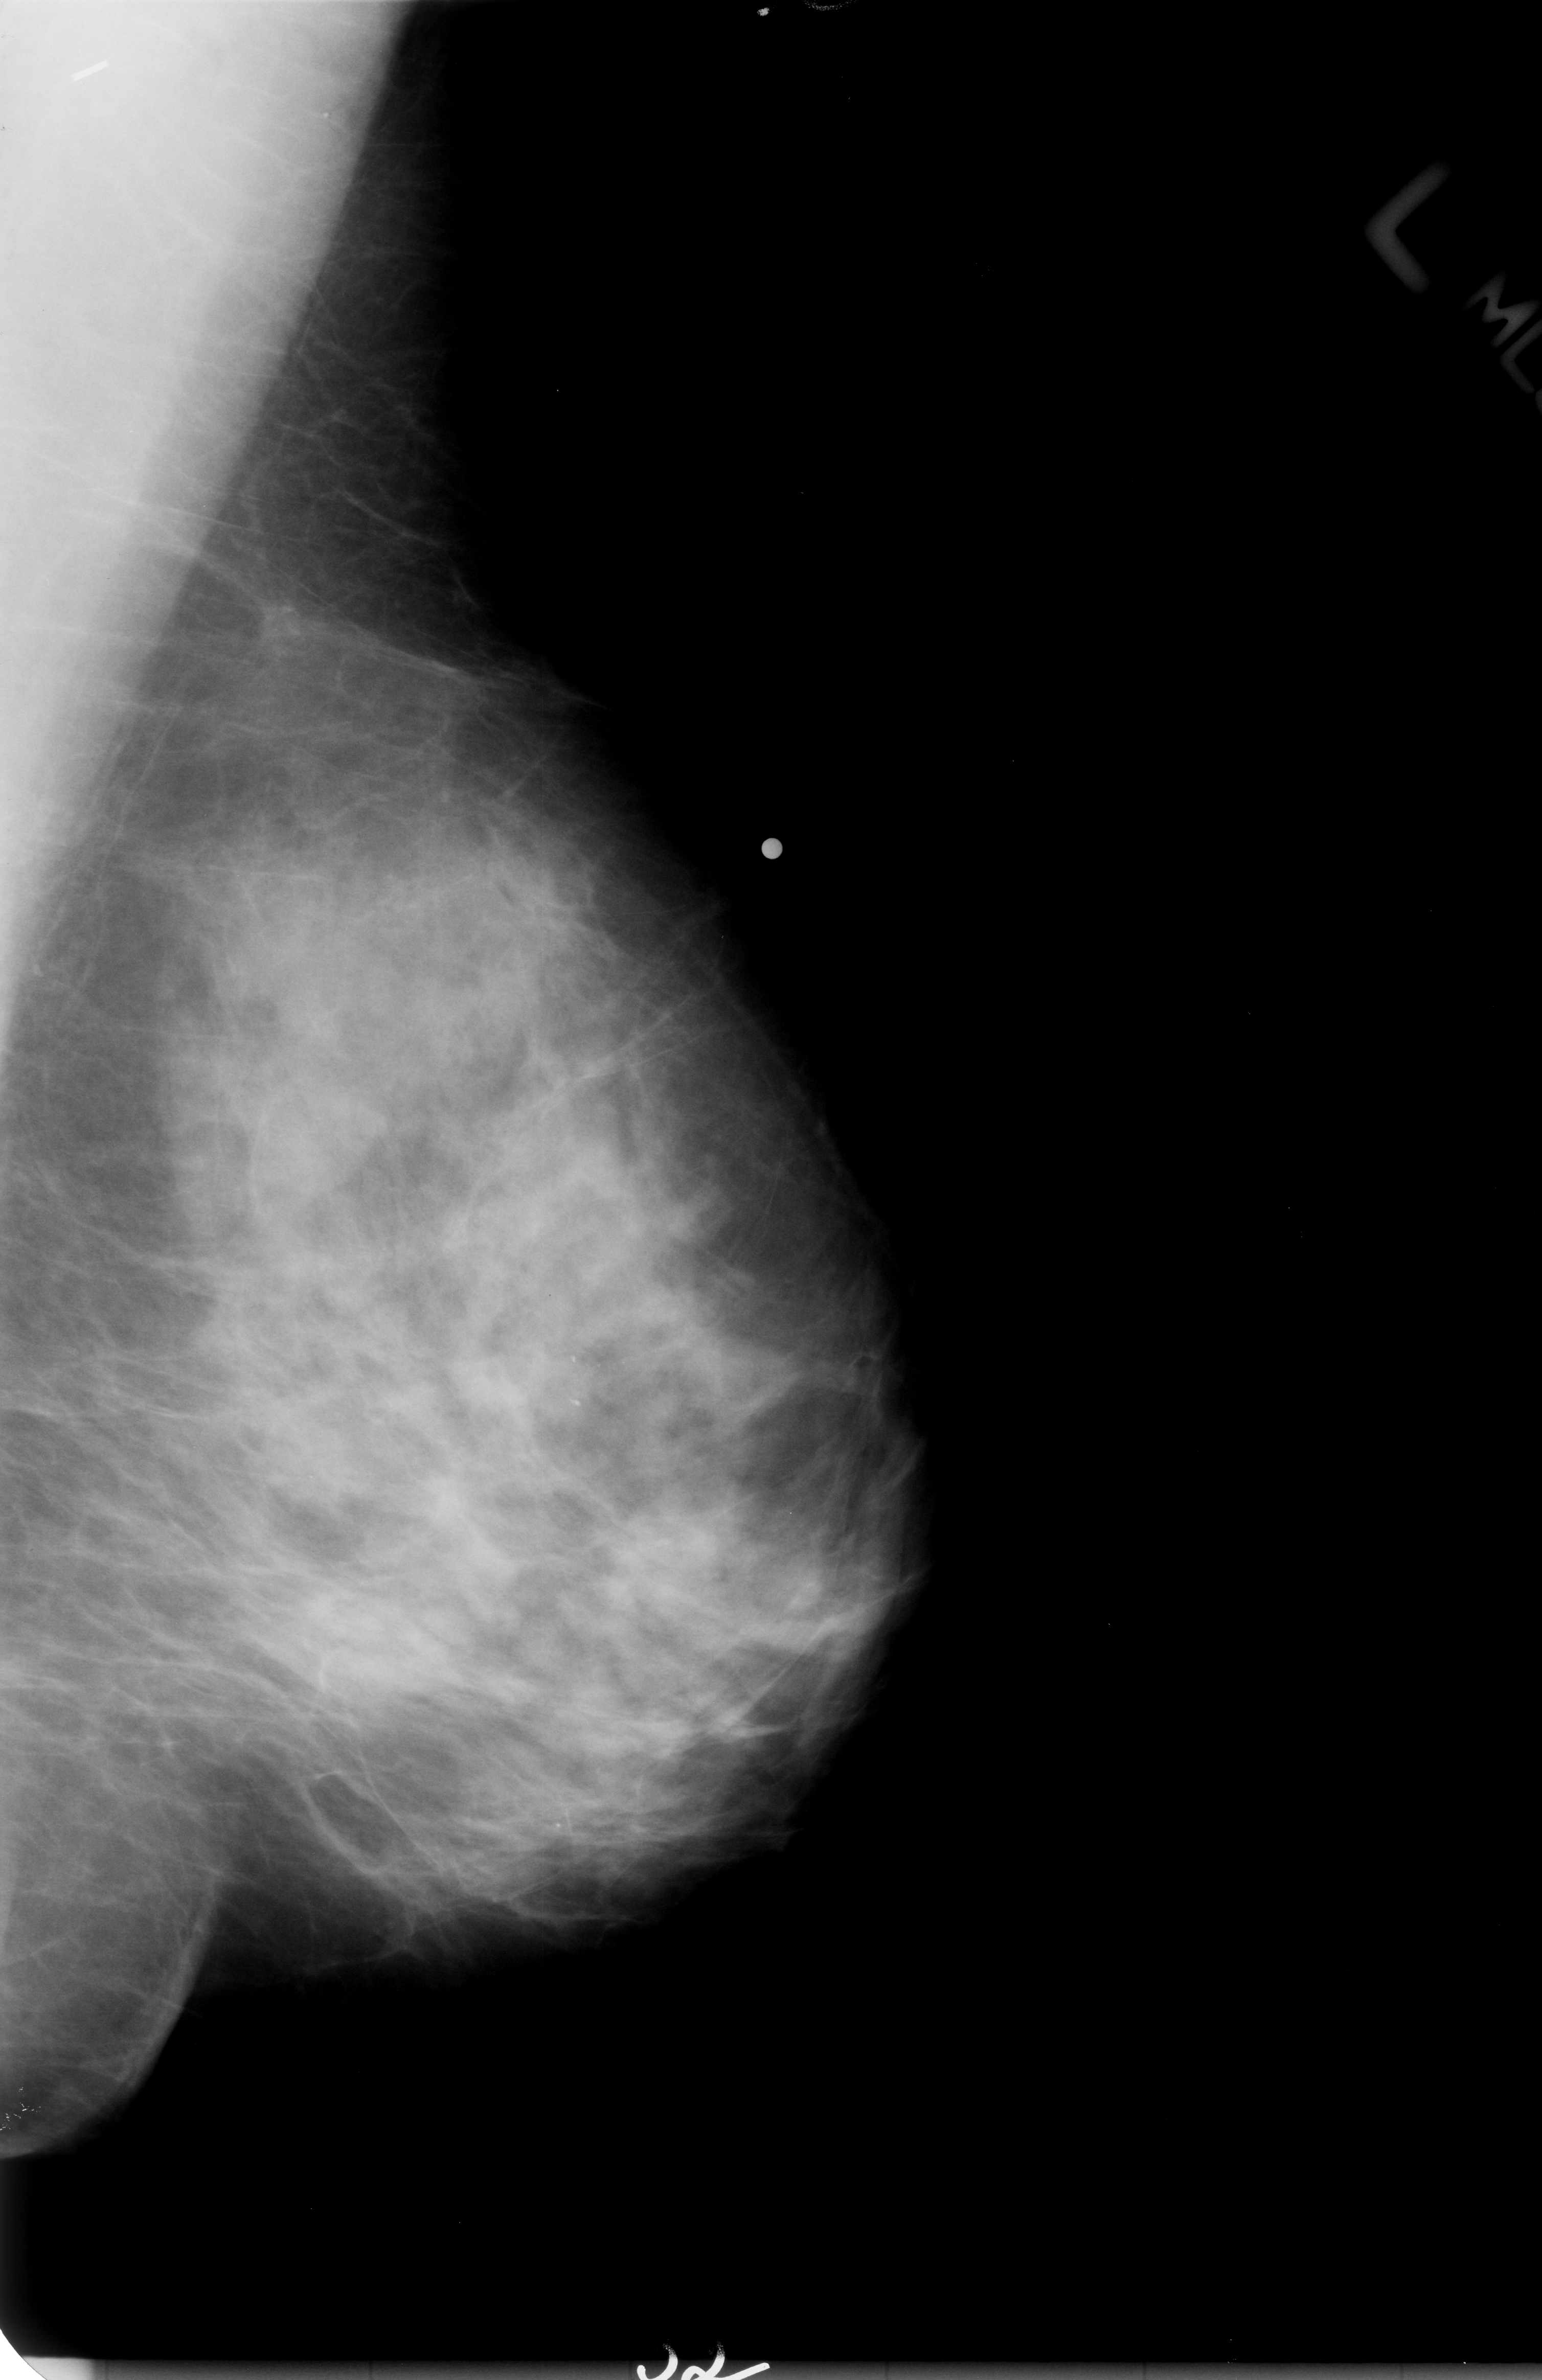
Digitized screen-film mammogram. Left breast. Mediolateral oblique (MLO) view. BI-RADS breast density category 3 (scale 1–4). 1542 × 2380 image matrix.
Marked abnormalities (boxes around the expert regions of interest):
- mass, shape irregular, margins obscured / ill defined; BI-RADS assessment category 3; subtlety rating 3 on a 1 (subtle) to 5 (obvious) scale; pathology result (as recorded, not read from the image): malignant: box from (x=225, y=1081) to (x=354, y=1202) px